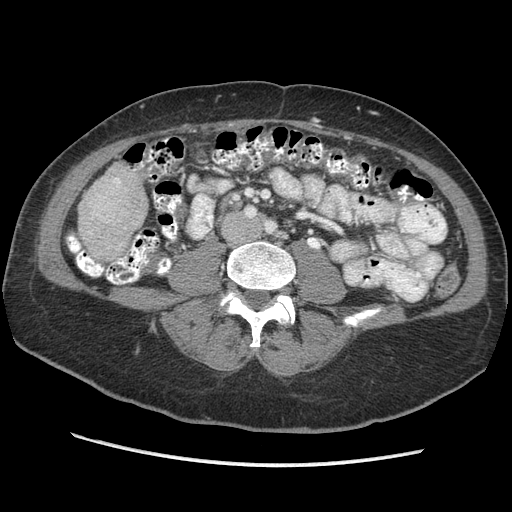
Contrast-enhanced abdominal CT (liver protocol), one axial slice; position 85 of 170 along the scan axis; reconstruction kernel STANDARD; soft-tissue window (W 400 / L 40 HU); 2.5 mm slice thickness; 512 × 512 image matrix, field of view 360 × 360 mm. Case-level facts recorded for this patient, not image findings: diagnosis: hepatocellular carcinoma (patient treated with transarterial chemoembolisation; whether this scan precedes or follows treatment is not stated here); TNM stage (as recorded): Stage-II; Child-Pugh class: A; tumour differentiation: no biopsy; tumour size: 4 cm.
Annotated regions visible in this slice (semi-automatically segmented with operator editing):
- liver parenchyma outside the tumour (the mass and vessels are separate outlines, so this box may not span the whole liver): bounding box [x1, y1, x2, y2] px = [78, 164, 148, 260]
- liver vessels: [97, 178, 121, 216]